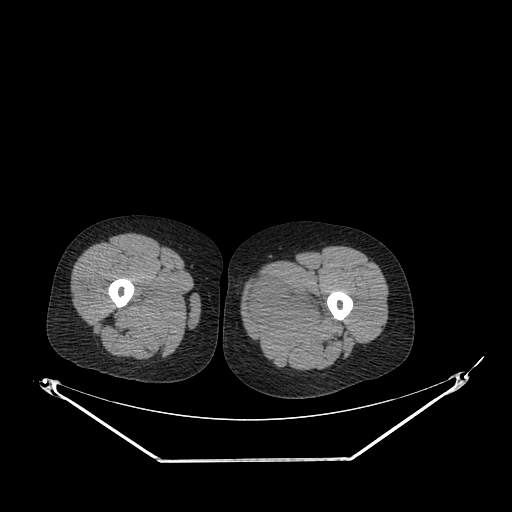
CT of an extremity soft-tissue mass (from a PET/CT study), one axial slice; position 228 of 267 along the scan axis; reconstruction kernel SOFT; 120 kVp; soft-tissue window (W 400 / L 40 HU); 3.75 mm slice thickness; 512 × 512 image matrix, field of view 500 × 500 mm. Female patient. From the clinical record (not read from this slice): histological type: pleiomorphic leiomyosarcoma; grade: intermediate; site of the primary tumour: left thigh.
Outlined on this slice (expert contour drawn on MRI and transferred to this co-registered scan by the dataset authors):
- gross tumour volume including surrounding oedema: bounding box [x1, y1, x2, y2] px = [247, 274, 328, 325]
- gross tumour volume (mass): [249, 276, 316, 325]